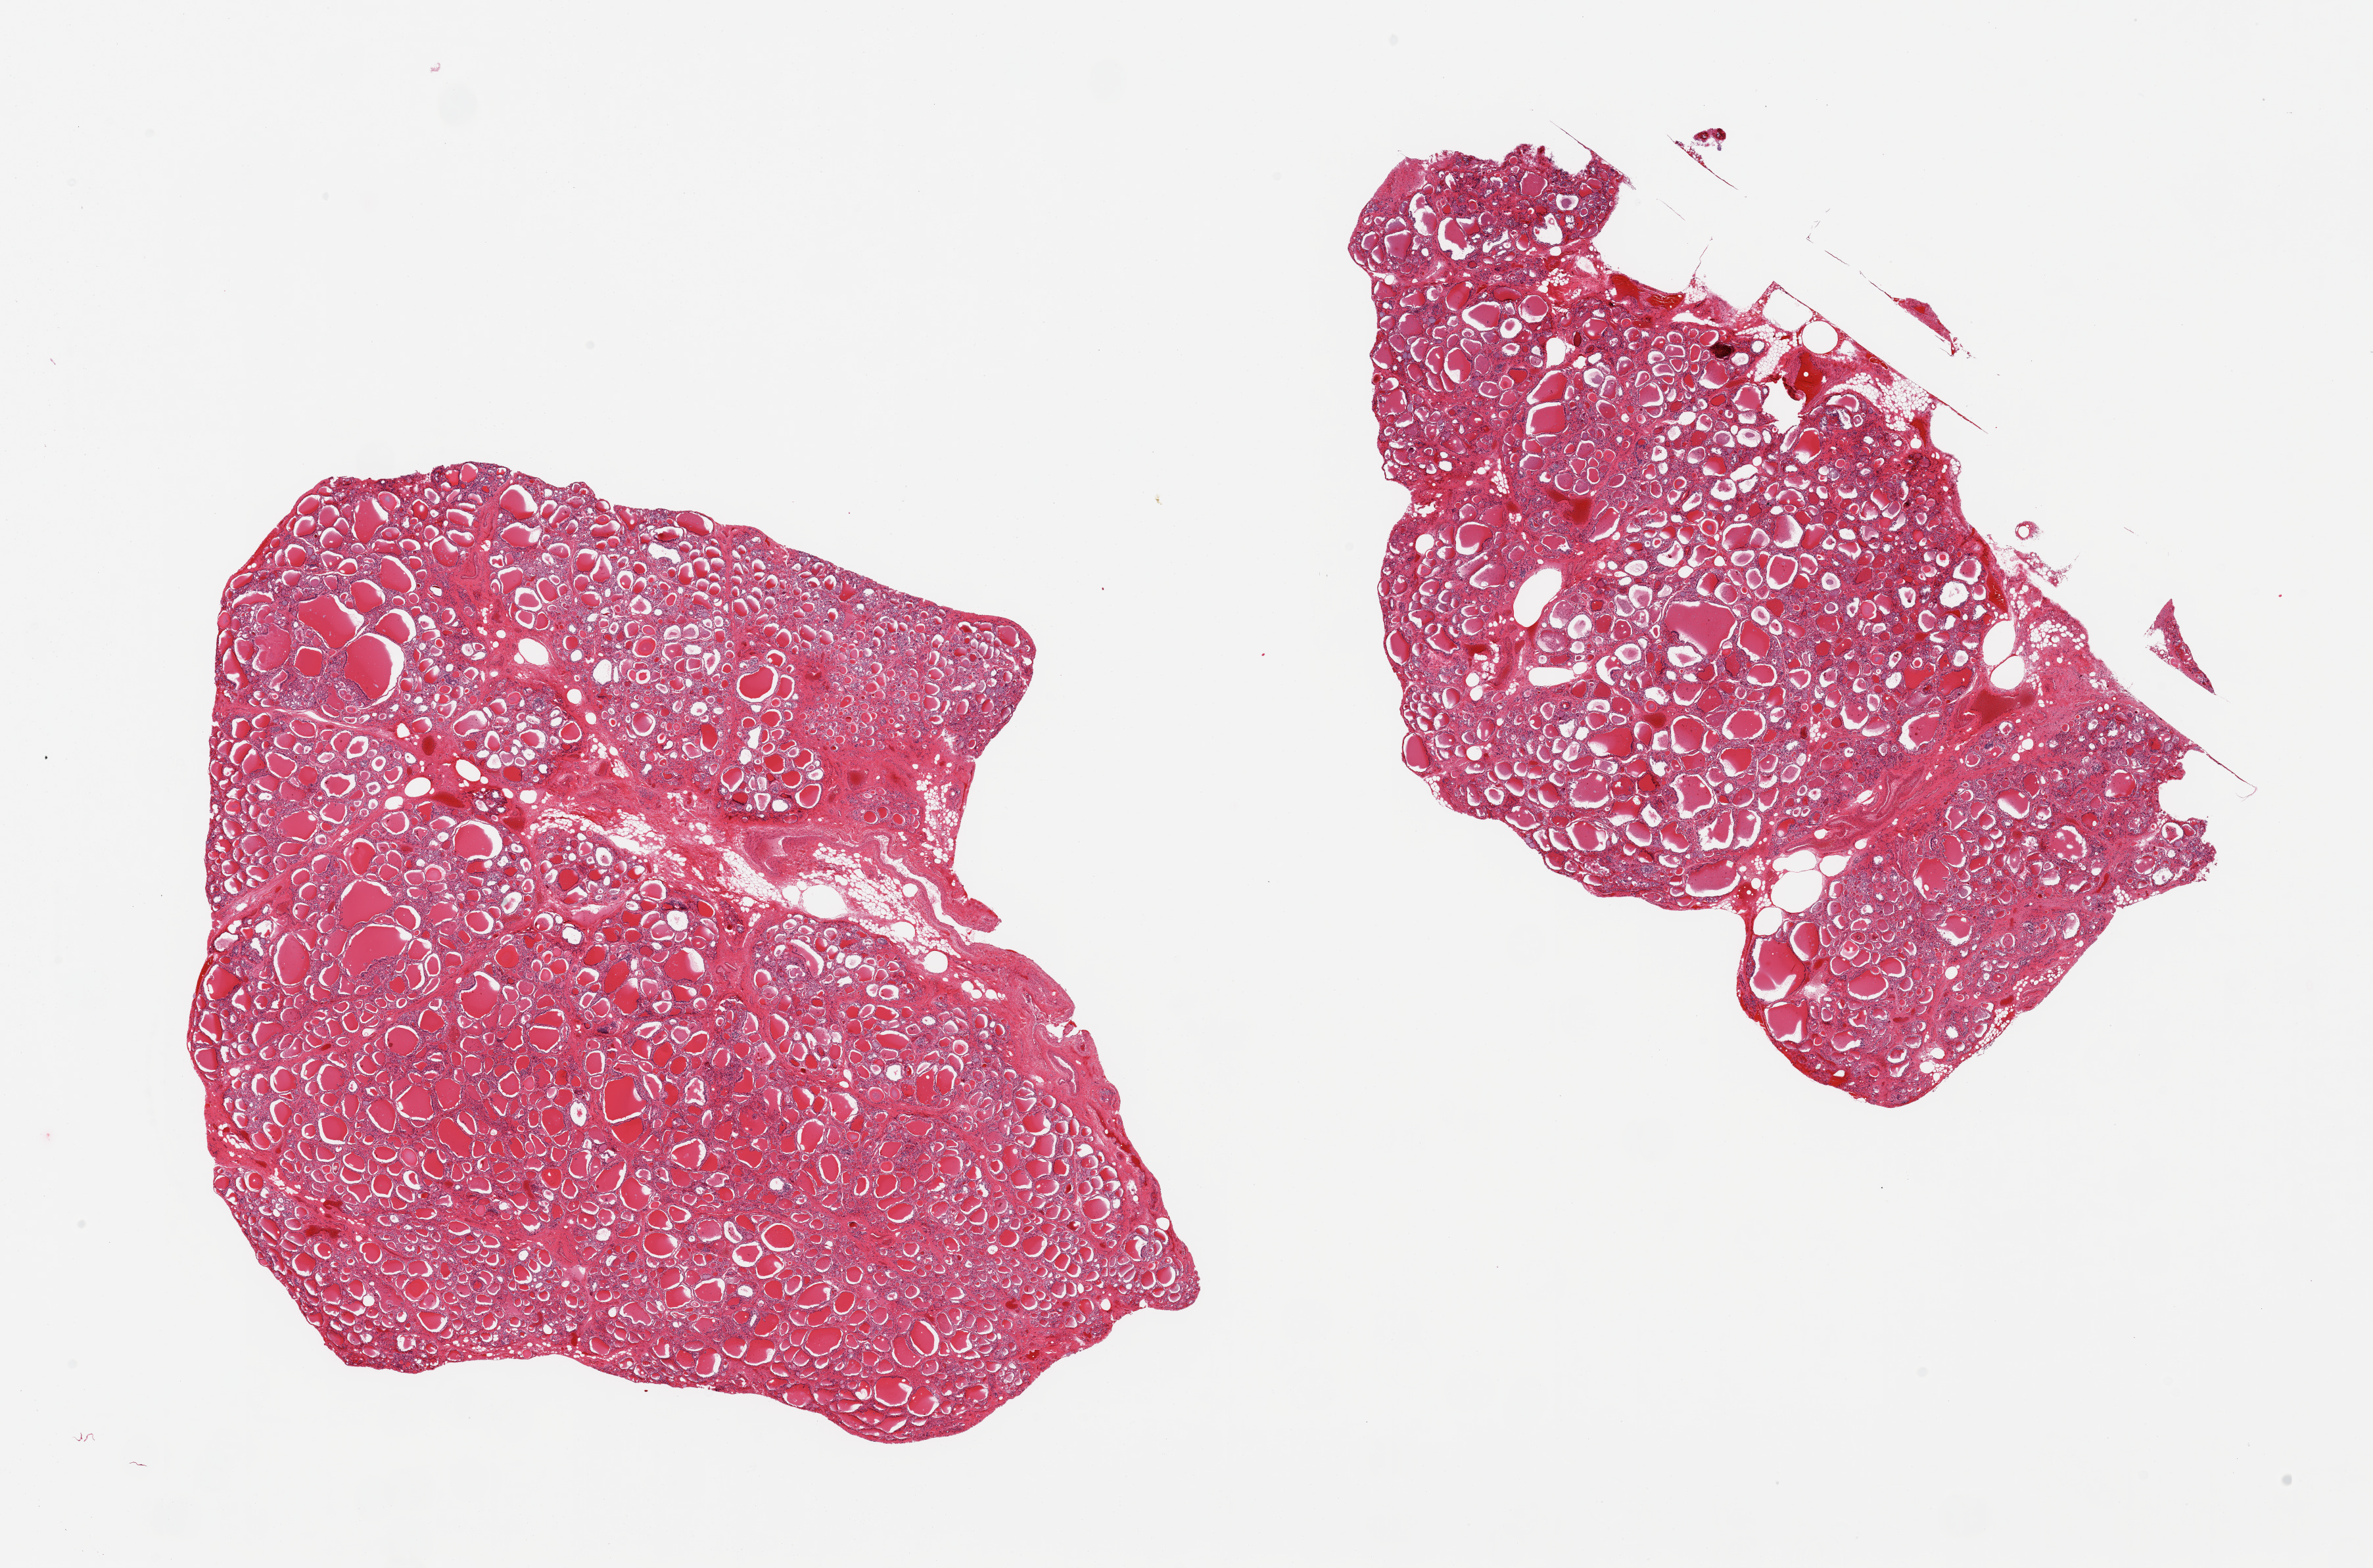
Digitized haematoxylin and eosin-stained section, brightfield, a low-resolution overview of the entire scanned area, about 28.5 x 18.9 mm (slide scanned at 20x), PAXgene-fixed paraffin-embedded (PFPE) section, sampled site (target tissue): thyroid, tissue donor sample.
Reviewer comment on this tissue sample: 2 pieces; no lesions.